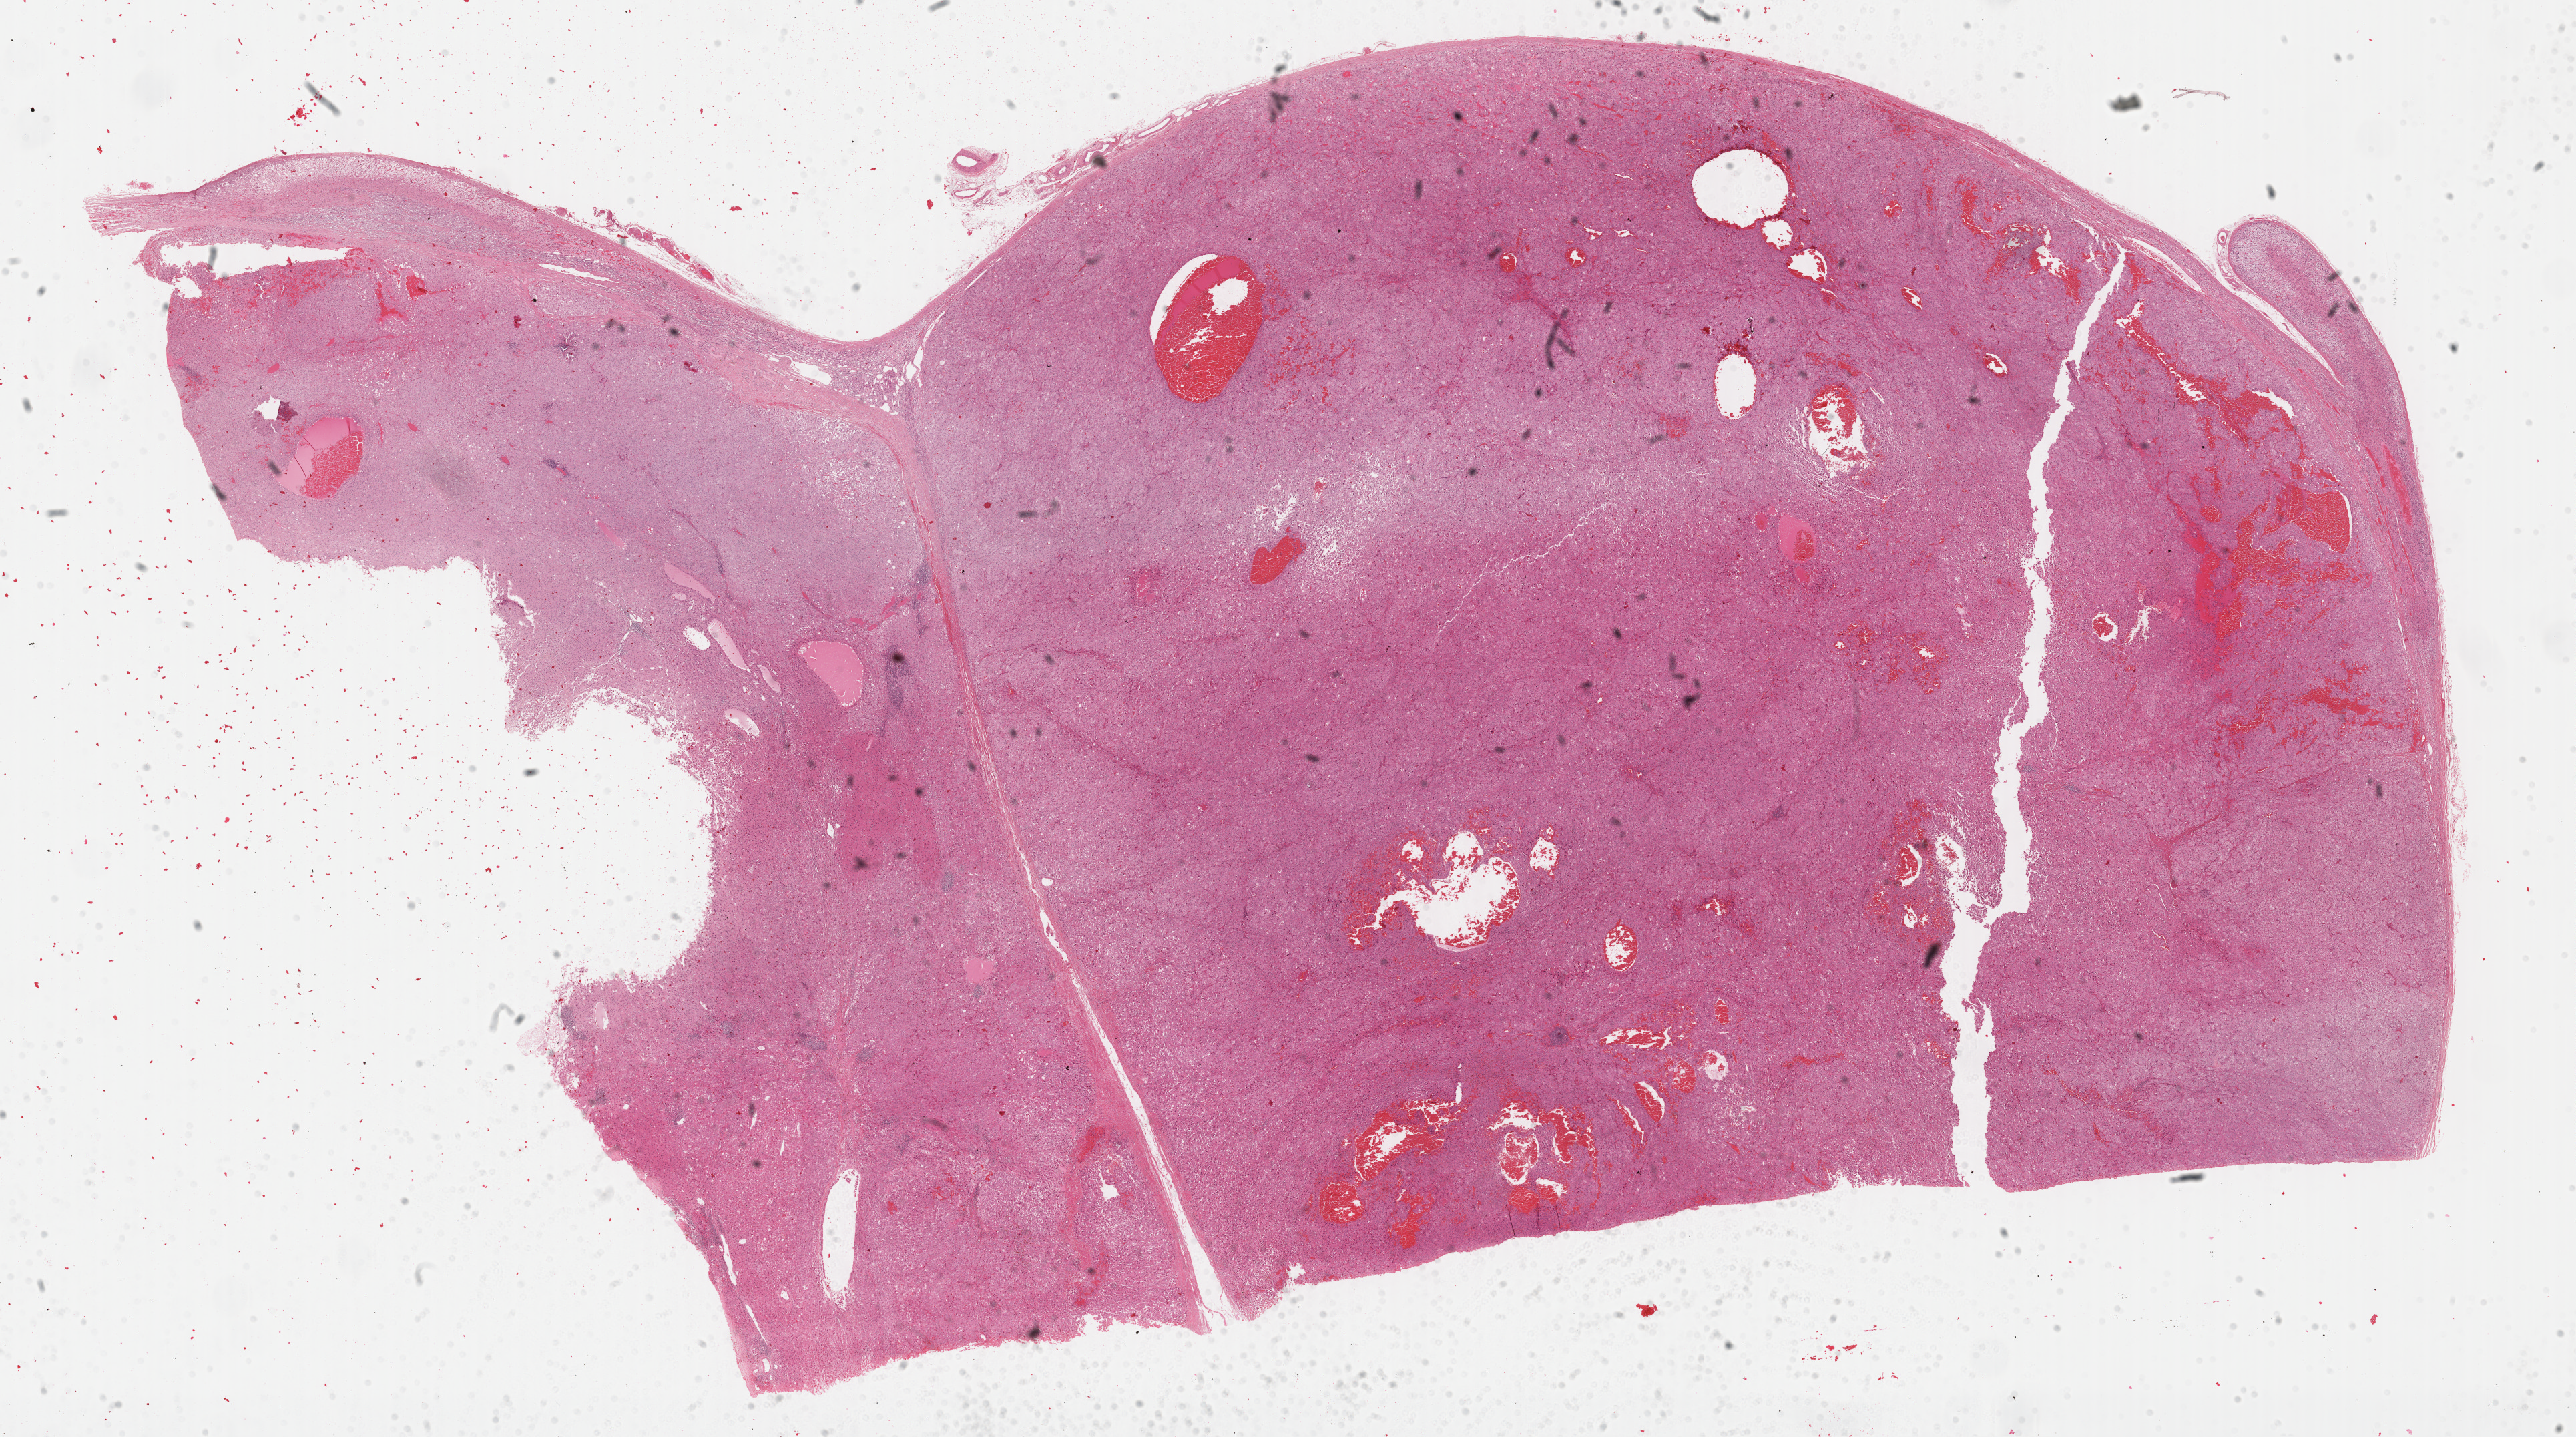
Whole-slide histology image, H&E-stained, whole scanned area (about 31.2 x 17.4 mm) shown as a low-resolution overview, FFPE section, primary tumour sample from the adrenal cortex. Male, age 22 years at initial diagnosis.
* pathologic diagnosis: Adrenal cortical carcinoma